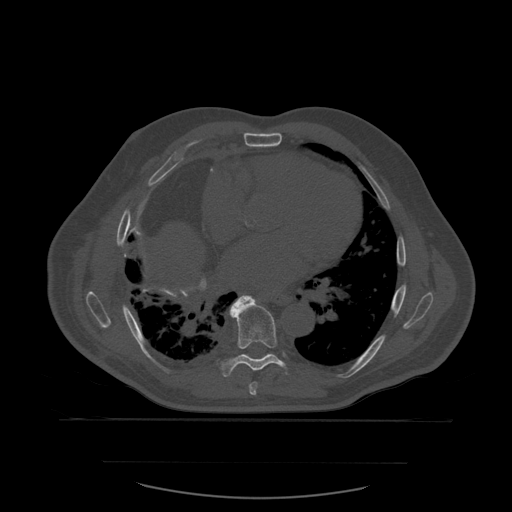
CT including the spine, one axial slice. Slice 362 of 590 in the series (ordered by position). Bone window (W 1800 / L 400 HU). 1.25 mm slice thickness. 512 × 512 image matrix, field of view 479 × 479 mm. Patient age 71 years. From the clinical record (not read from this slice): primary cancer: lung; vertebrae with lytic lesions (as recorded): T1, T2, L5, S1.
Annotated regions visible in this slice (semi-automatically segmented with operator editing):
- T7 vertebra: bounding box <249,382,258,396> (left, top, right, bottom; pixels)
- T8 vertebra: <219,296,290,377>